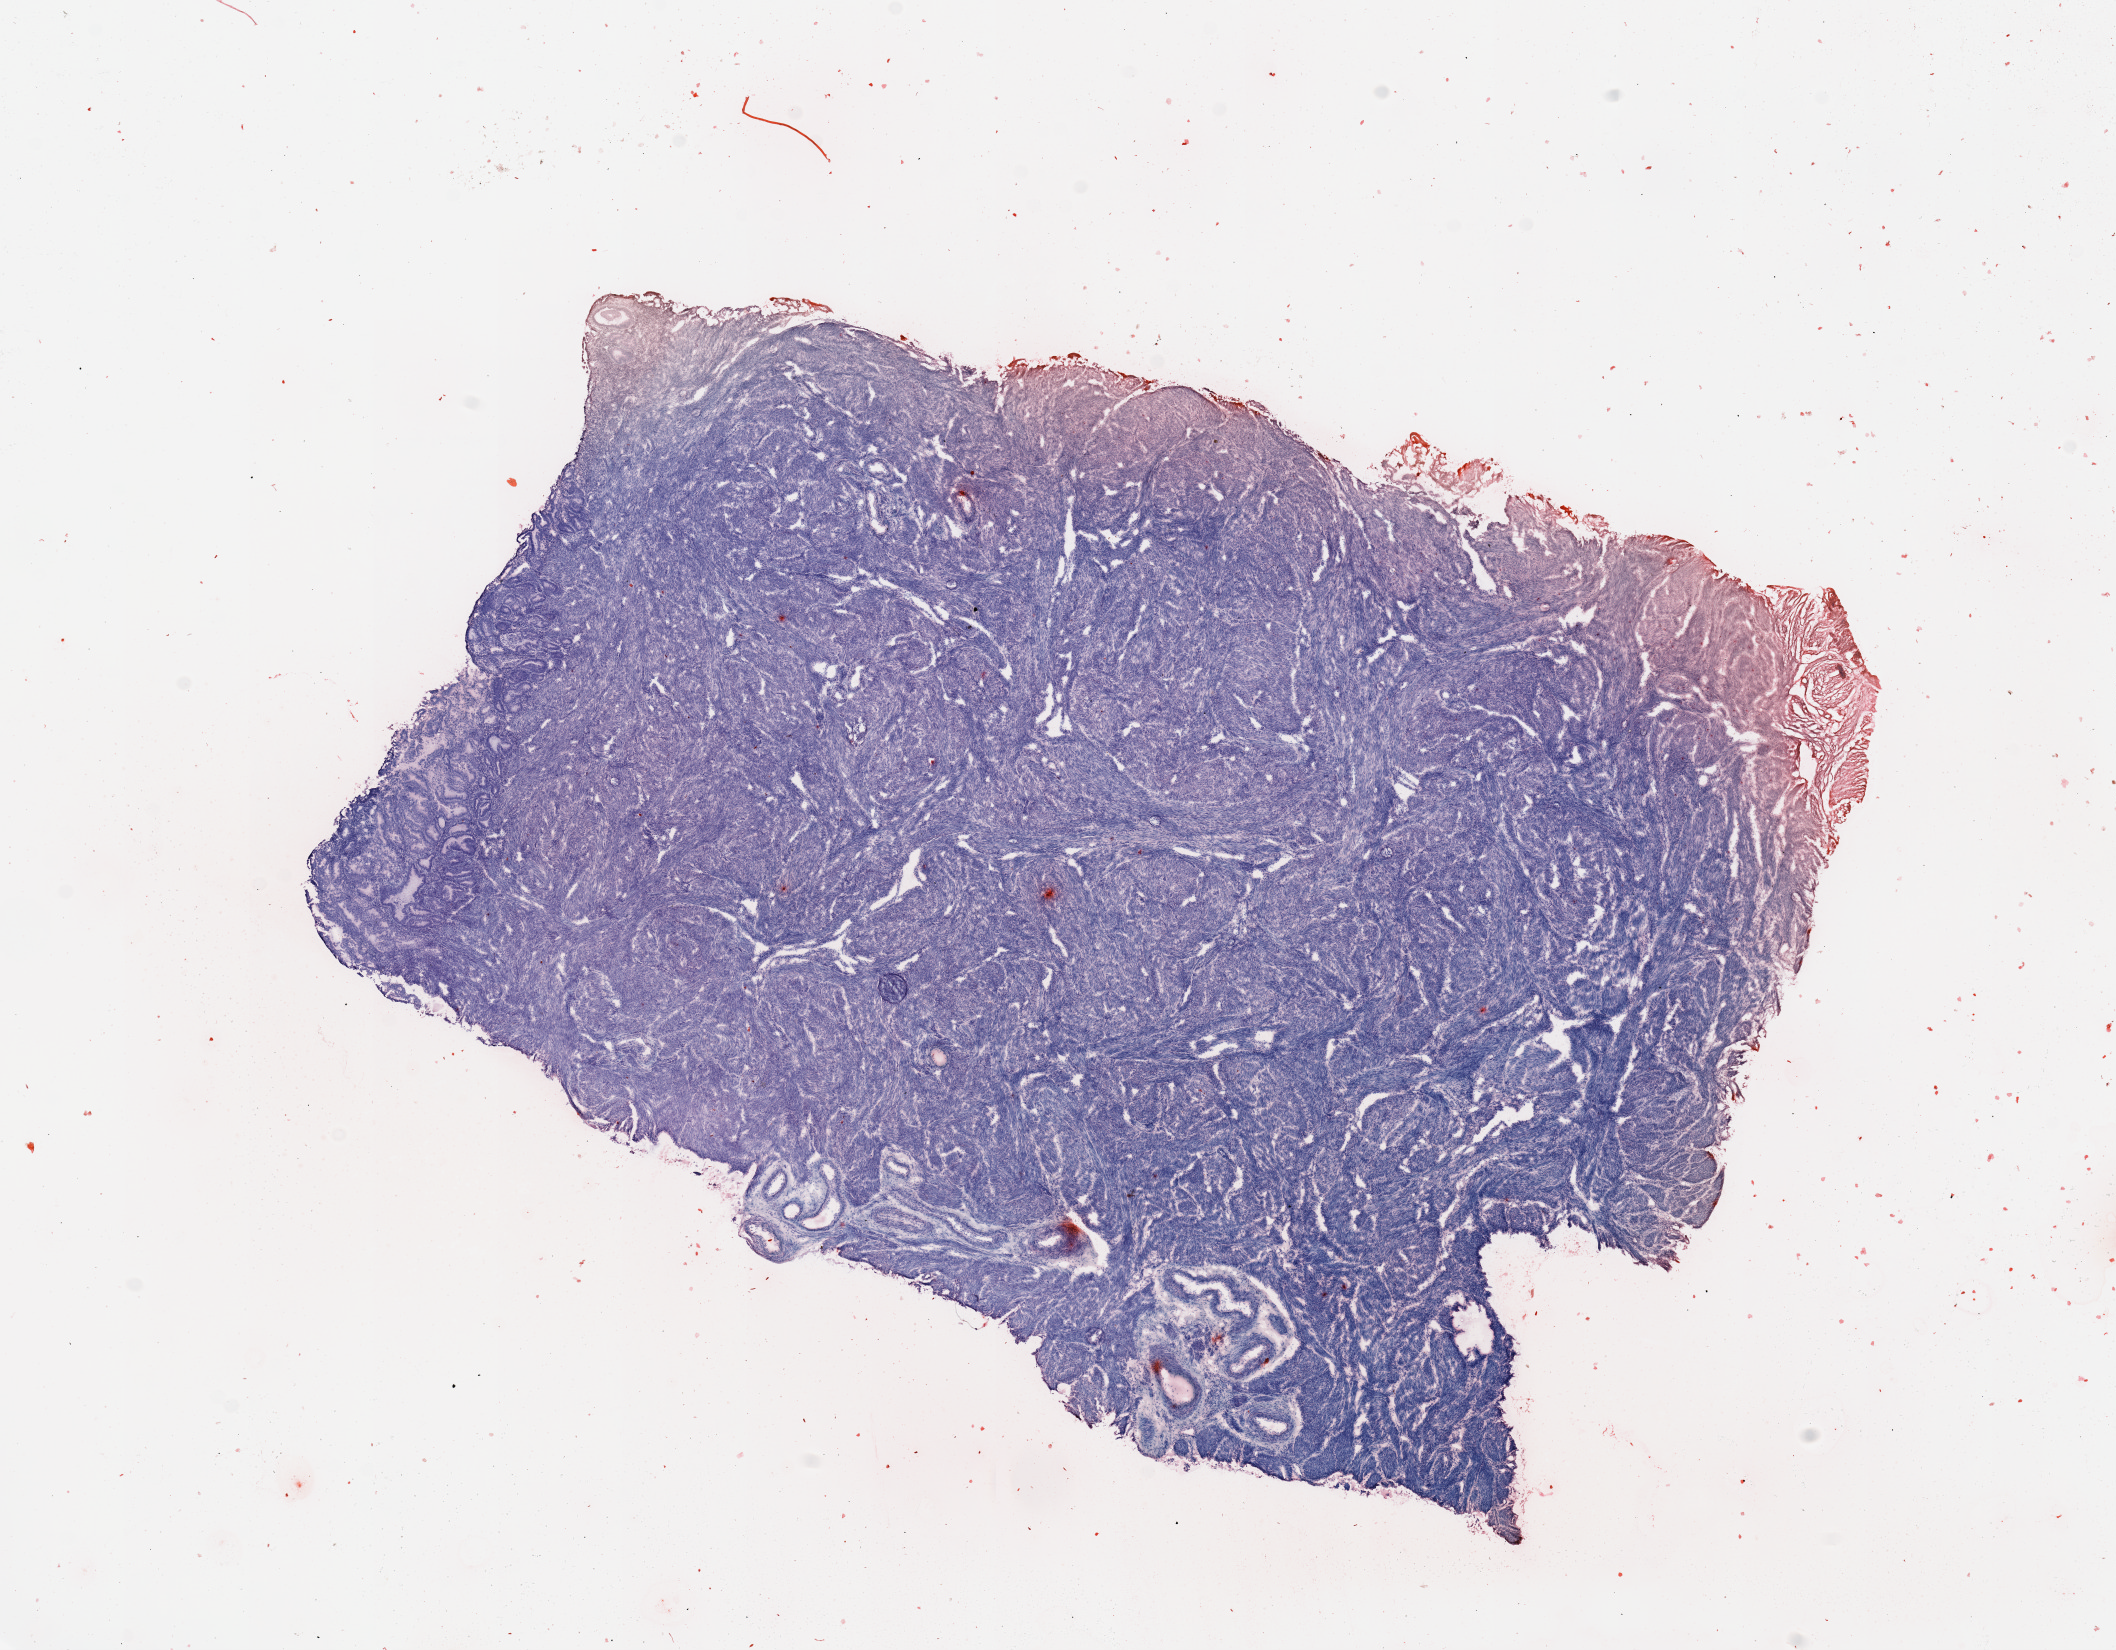
Whole-slide histology image, H&E, a low-resolution overview of the entire scanned area, about 16.7 x 13.0 mm, normal (non-tumour) tissue sample, sampled site: uterus. Female, 61 y/o.
This section: normal (non-tumour) tissue from the same patient. Patient diagnosis: Endometrioid adenocarcinoma, NOS.